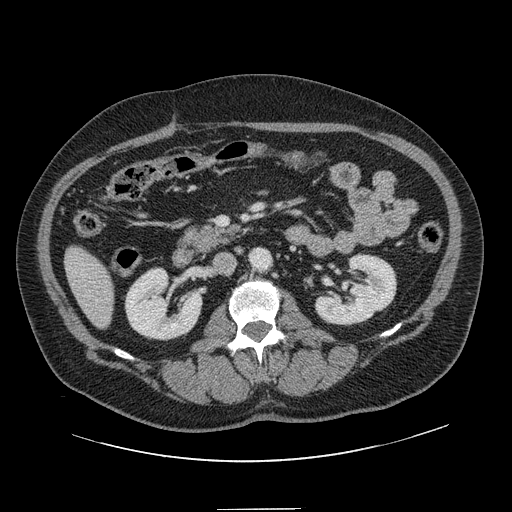
Contrast-enhanced abdominal CT, one axial slice. Slice 43 of 154 in the series (ordered by position). 120 kVp. Intravenous contrast given. Soft-tissue window (W 400 / L 40 HU). 512 × 512 image matrix, field of view 451 × 451 mm. Male patient, age 61 years. From the clinical record (not read from this slice): diagnosis: colorectal cancer liver metastases, imaged before liver resection; multiple liver metastases: yes; largest metastasis: 2.6 cm.
Outlined on this slice (expert manual segmentation):
- liver: bounding box (x1, y1, x2, y2) in pixels: (66, 248, 113, 327)
- planned liver remnant (the part of the liver to remain after resection): (66, 248, 113, 327)